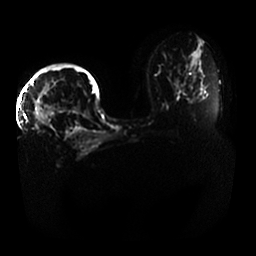
Breast MRI, one axial slice. Slice 21 of 33 in the series (ordered by position). Diffusion-weighted series; image 2 of 4 stored at this slice position (different b-values; order by instance number). 1.5 T. 256 × 256 image matrix. Female patient.
Structures marked on this image (outlined manually by an expert reader):
- tumour on diffusion-weighted imaging: bounding box (x1, y1, x2, y2) in pixels: (34, 109, 53, 125)